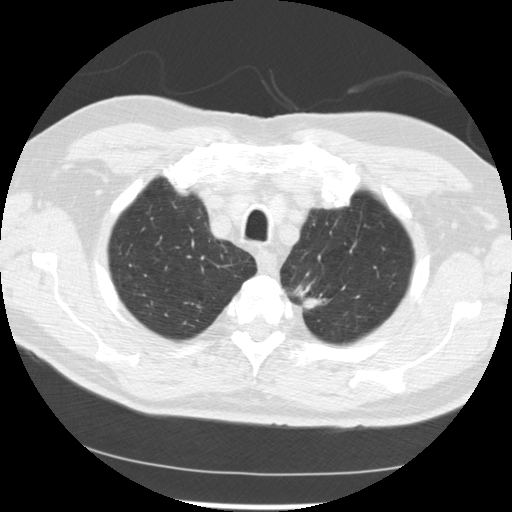
Low-dose screening chest CT, one axial slice; 120 kVp; lung window (W 1500 / L -600 HU); 2.5 mm slice thickness; 512 × 512 image matrix, field of view 341 × 341 mm.
Annotated regions visible in this slice (expert manual segmentation):
- lesion 2 (tumor, upper lobe of left lung): bounding box [x1, y1, x2, y2] px = [303, 298, 324, 309]